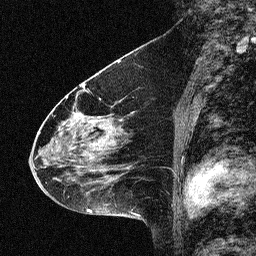
Breast MRI (dynamic contrast-enhanced), one sagittal slice; slice 31 of 64 in the series (ordered by position); dynamic contrast-enhanced study with each time point stored as its own series, time point 2 of 3 at this slice position (early post-contrast, ordered by acquisition time); 1.5 T; TE 4.5 ms, TR 11 ms; 2.06 mm slice thickness; 256 × 256 image matrix. Female patient, age 46 years. From the clinical record (not read from this slice): setting: breast cancer imaged before/during neoadjuvant chemotherapy; receptor status: HER2-positive.
Outlined on this slice (semi-automatic segmentation, software-assisted and operator-edited):
- analysis volume of interest (the breast-tissue region the enhancement analysis was run in; not a lesion): box from (x=42, y=80) to (x=150, y=180) px
- tumour enhancement mask (voxels above the 90 % enhancement threshold inside the analysis volume of interest): (x=43, y=86)–(x=108, y=179)